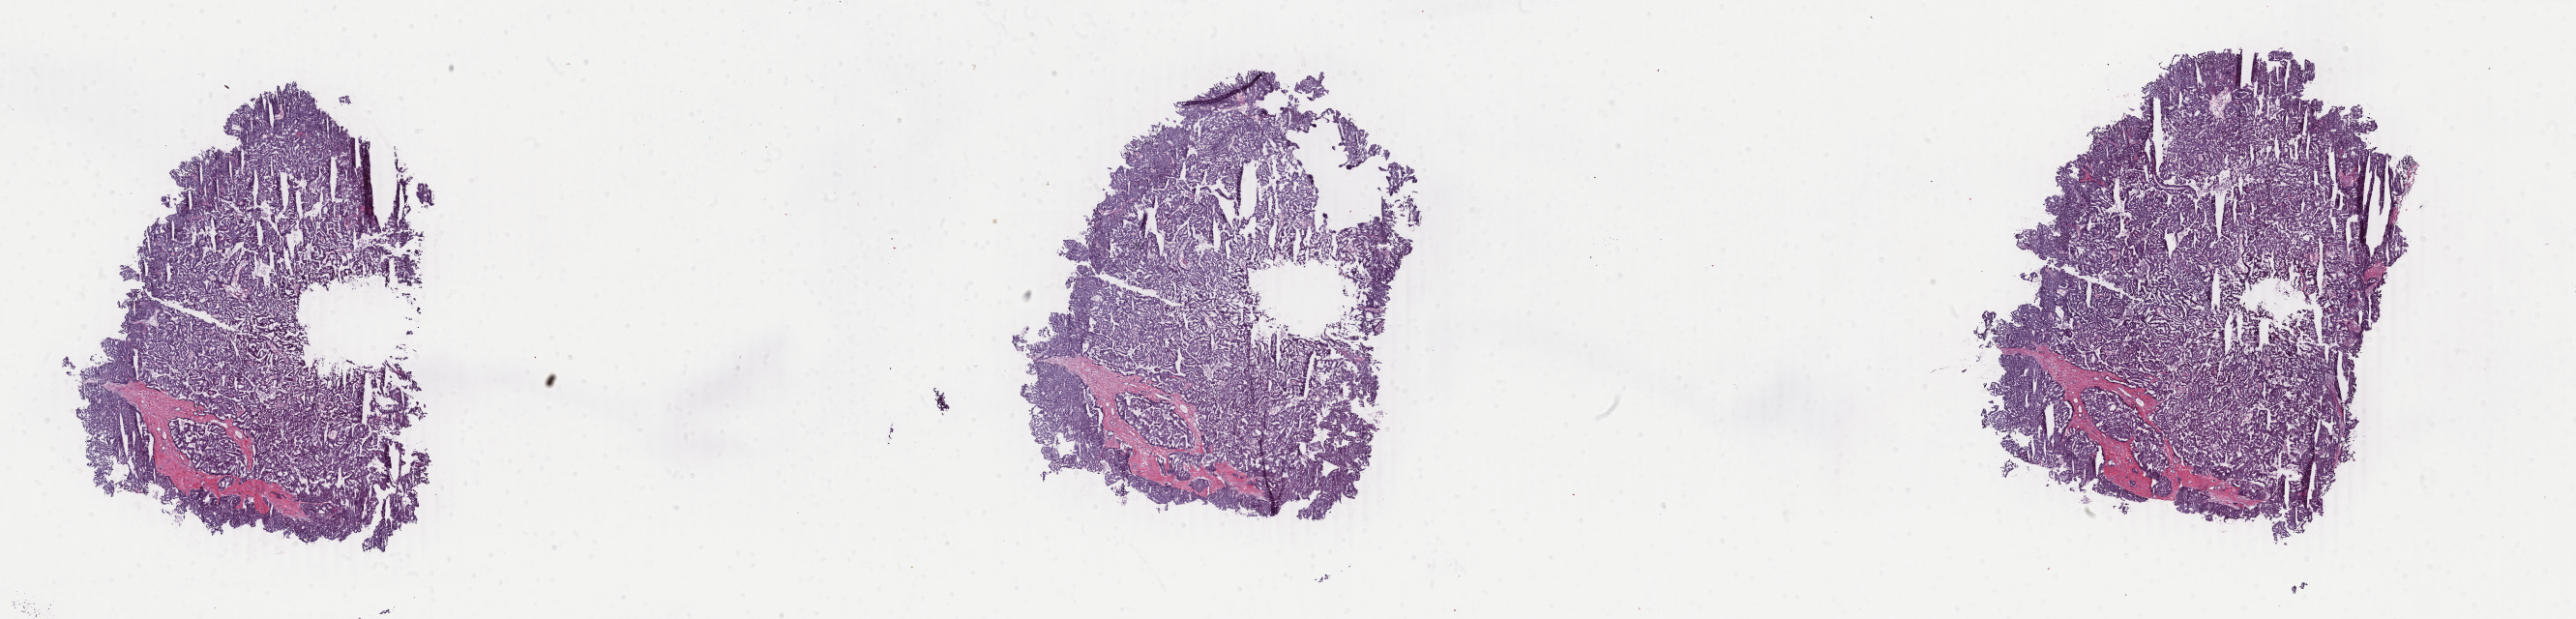
Whole-slide histology image, H&E, low-resolution overview of the scanned area, about 42.4 x 10.2 mm. Frozen section from the top of the tissue portion. Primary tumour sample from the breast. Female, age 62 years at initial diagnosis. Pathologist review of this section (percent, as recorded): tumour cells 90%, tumour nuclei 90%, normal cells 0%, stromal cells 8%, necrosis 2%. Inflammatory infiltration, as recorded: lymphocyte infiltration 1%, monocyte infiltration 0%, neutrophil infiltration 0%.
AJCC pathologic stage: IV (3rd edition). Laterality: left. Diagnosis: Infiltrating duct carcinoma, NOS.